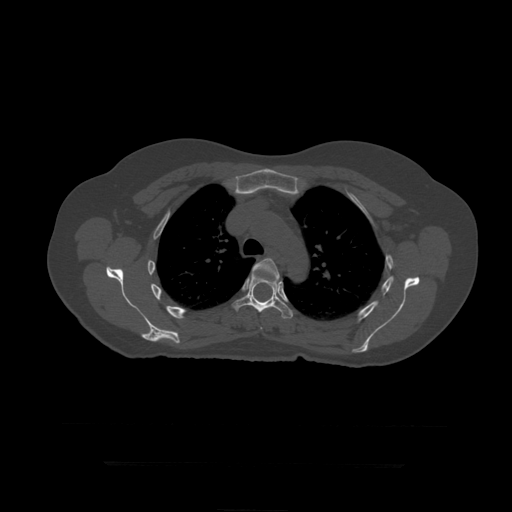
CT including the spine, one axial slice; position 324 of 399 along the scan axis; reconstruction kernel STANDARD; 120 kVp; bone window (W 1800 / L 400 HU); 512 × 512 image matrix, field of view 450 × 450 mm. Patient age 41 years. From the clinical record (not read from this slice): primary cancer: breast.
Structures marked on this image (semi-automatically segmented with operator editing):
- T5 vertebra: bounding box <252,259,280,330> (left, top, right, bottom; pixels)
- T6 vertebra: <231,275,294,319>